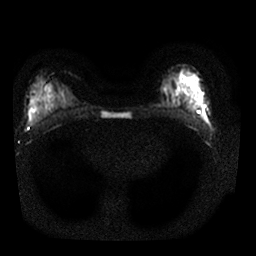
Breast MRI, one axial slice. Position 11 of 25 along the scan axis. Diffusion-weighted series; image 2 of 4 stored at this slice position (different b-values; order by instance number). 1.5 T. 4 mm slice thickness. 256 × 256 image matrix, field of view 320 × 320 mm. Female patient.
Annotated regions visible in this slice (outlined manually by an expert reader):
- tumour on diffusion-weighted imaging: bounding box [x1, y1, x2, y2] px = [193, 103, 198, 108]